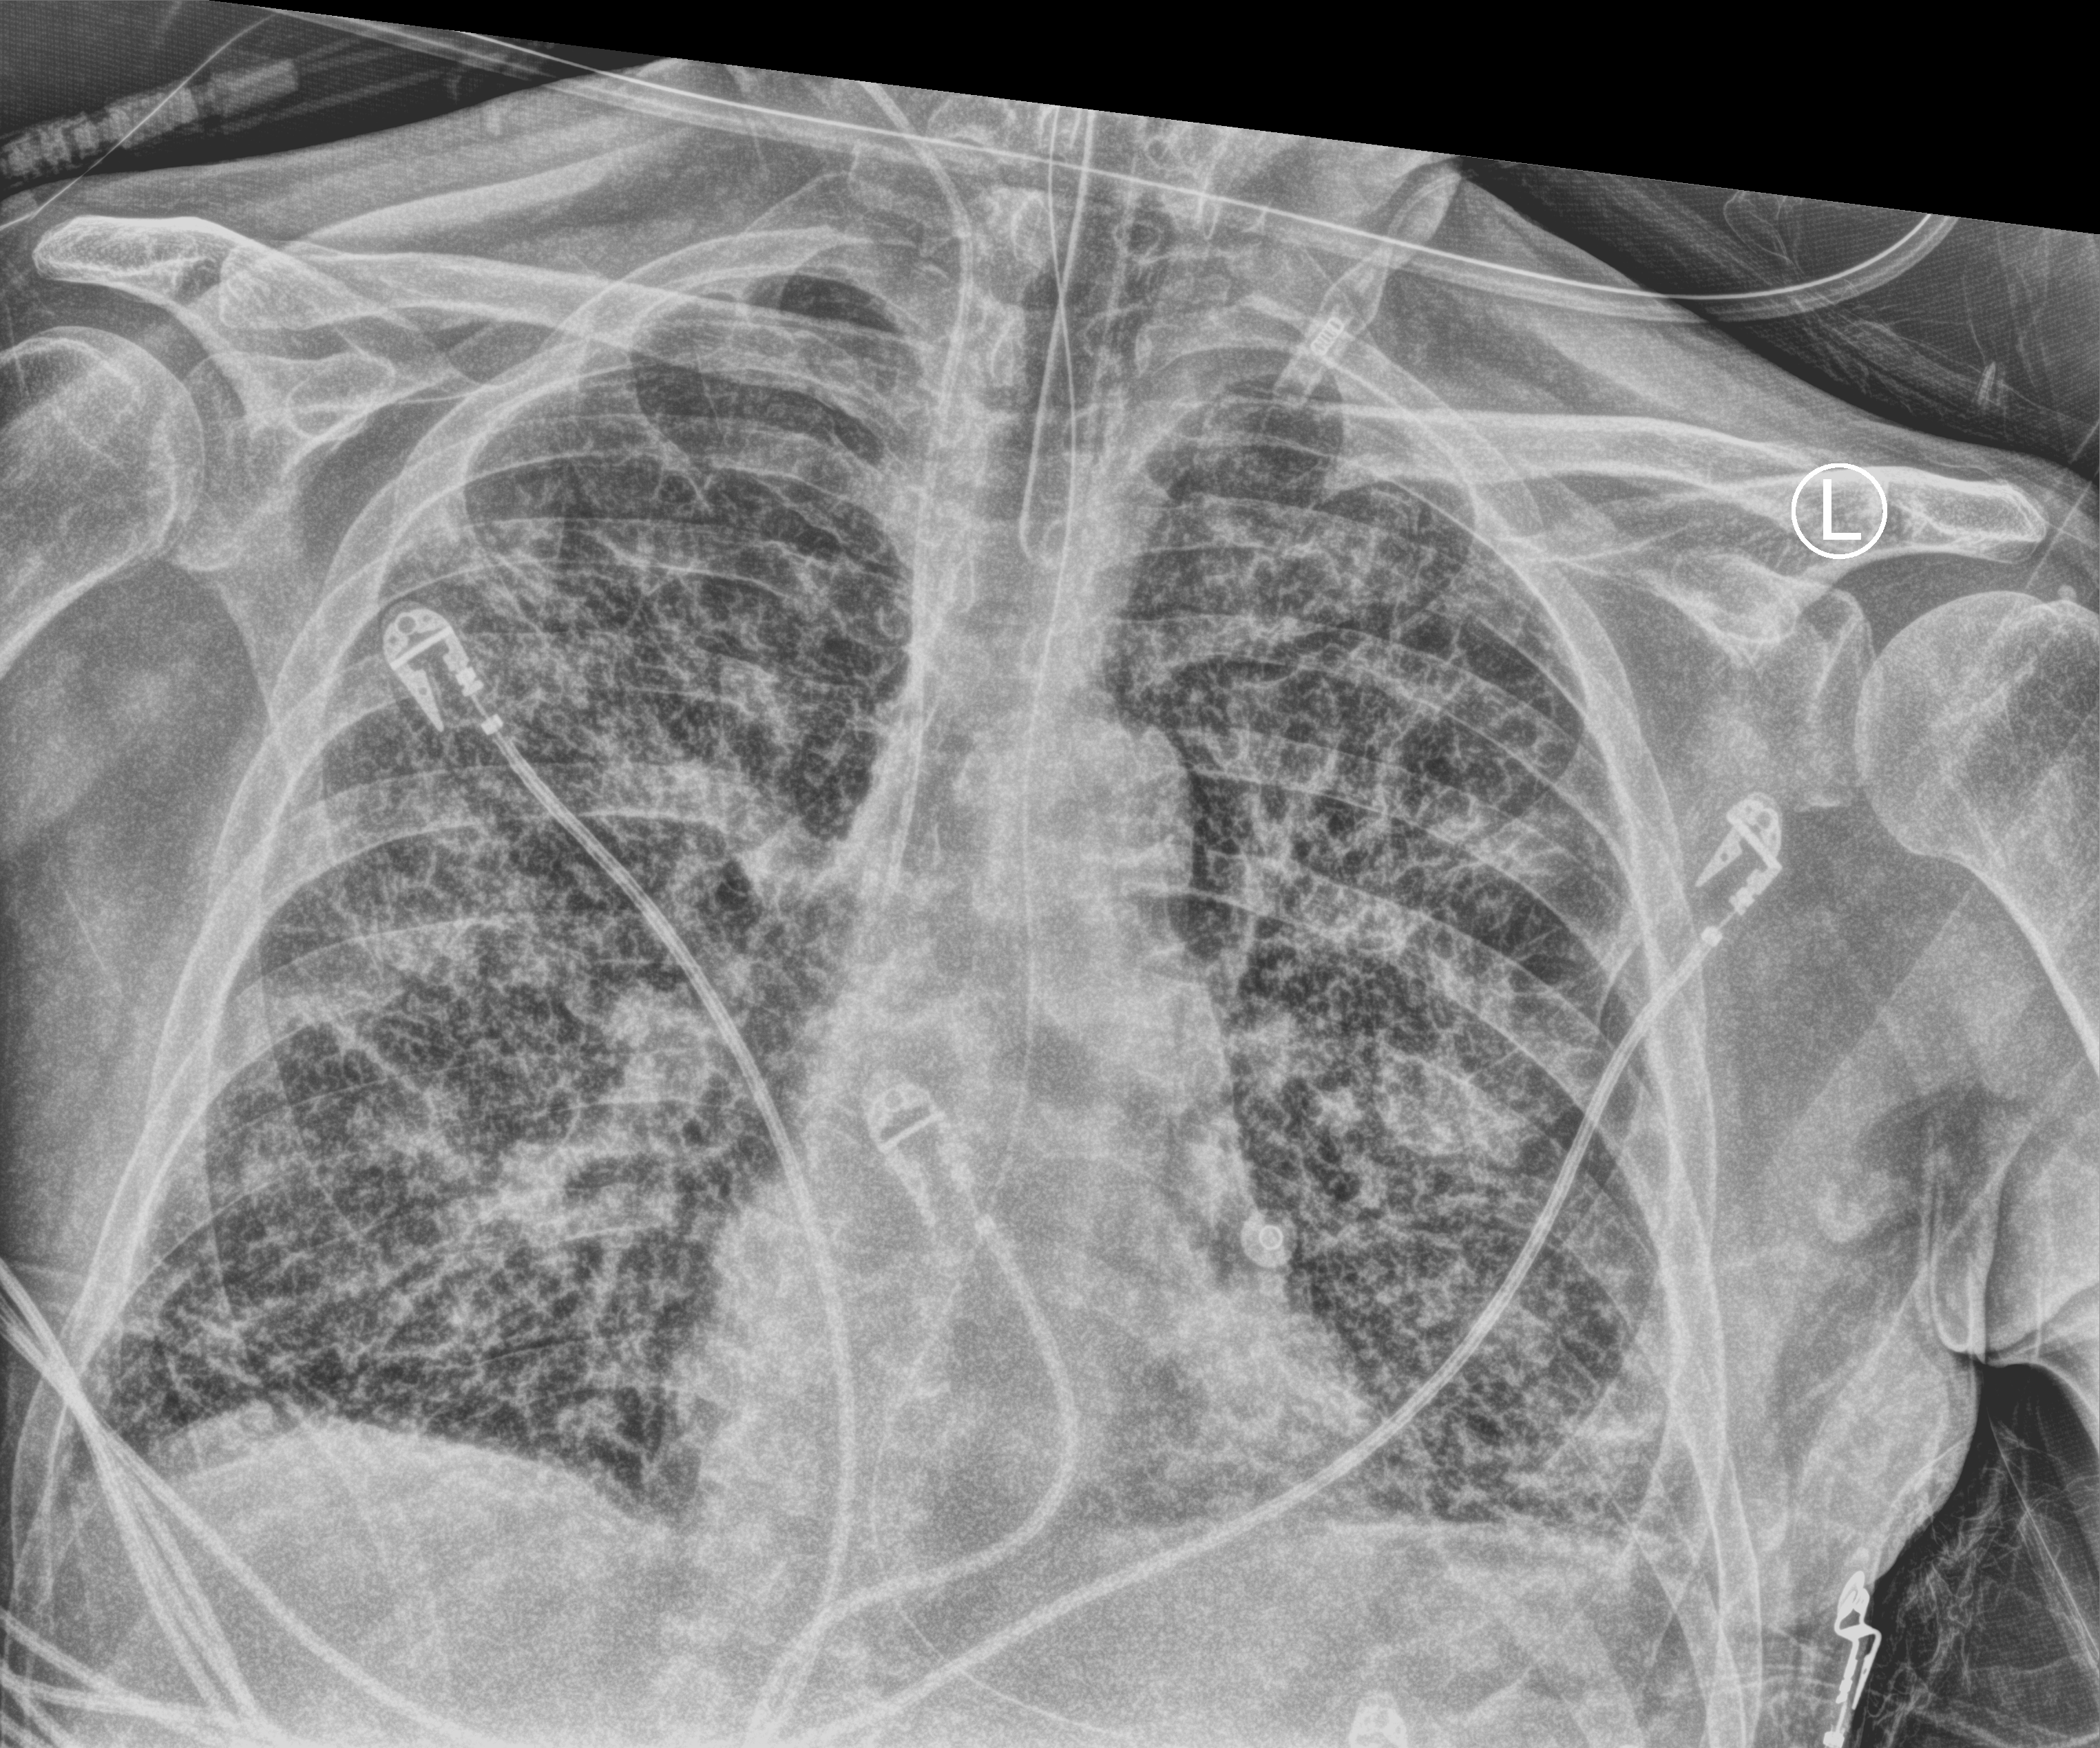
Chest X-ray (portable), anteroposterior (AP) projection. Male patient hospitalised with COVID-19, age 75–90 years.
From the hospital-stay record, not from the radiograph (when in the stay this image was taken is not recorded): admitted to intensive care during this hospital stay: yes.